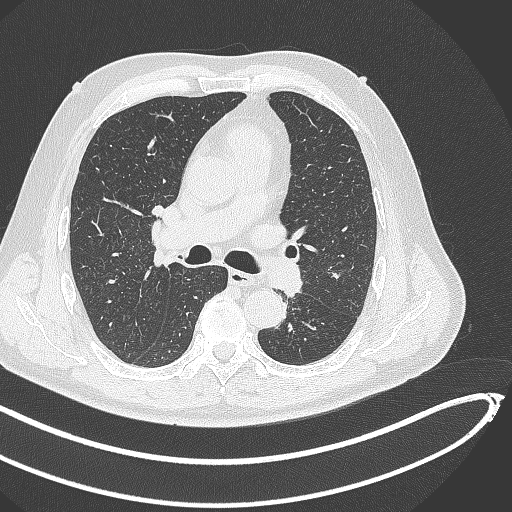
Chest CT, one axial slice. Position 279 of 468 along the scan axis. Reconstruction kernel B70f. Lung window (W 1500 / L -600 HU). 1 mm slice thickness. 512 × 512 image matrix, field of view 400 × 400 mm. Patient: male, 64 years. From the clinical record (not read from this slice): clinical TNM (as recorded): T1c N0 M0; histopathological grade: G2.
Annotated regions visible in this slice (rectangle marked by the reading radiologist):
- lung tumour (recorded histology: squamous cell carcinoma): bounding box [x1, y1, x2, y2] px = [265, 252, 310, 297]